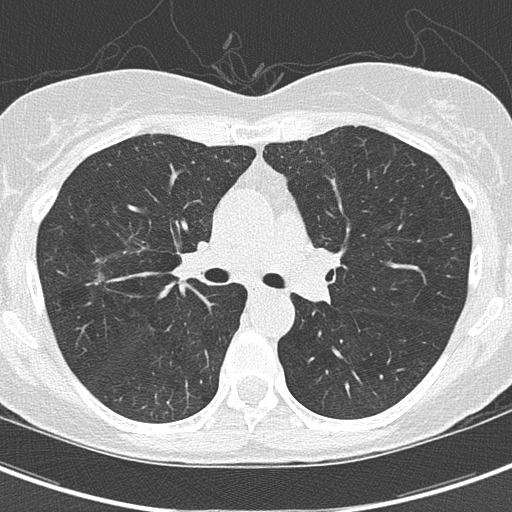
Low-dose screening chest CT, axial slice; third screening round (two years after baseline); lung window (W 1500 / L -600 HU); 2 mm slice thickness; lung (sharp) reconstruction kernel (B50f); 120 kVp; slice 59 of 154 in the series. Female, age 59 years at enrolment. Current smoker at enrolment.
- Expert reader's lesion annotation, bounding box (x1, y1, x2, y2) in pixels: (71, 260, 132, 317).
- Reader record for this screening exam (exam-level; its link to the box is not recorded): non-calcified nodule or mass ≥4 mm, right upper lobe, 10 × 8 mm, poorly defined margins, ground glass attenuation, pre-existing on the prior screen: yes; interval growth: yes.
- Later outcome: lung cancer diagnosed 63 days after this screen — bronchiolo-alveolar adenocarcinoma, NOS, right upper lobe, well differentiated (G1), stage IA (AJCC 6th edition), 4 mm at pathology.